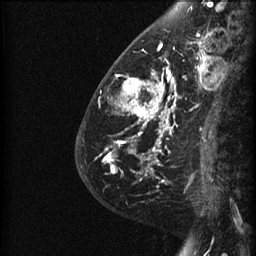
Breast MRI (dynamic contrast-enhanced), one sagittal slice; position 16 of 60 along the scan axis; dynamic contrast-enhanced series, image 2 of 3 at this slice position (ordered by acquisition); 1.5 T; TE 4.2 ms, TR 22.7 ms; 1.5 mm slice thickness; 256 × 256 image matrix. Female patient, age 48 years. Case-level facts recorded for this patient, not image findings: setting: breast cancer imaged before/during neoadjuvant chemotherapy; receptor status: triple-negative.
Structures marked on this image (semi-automatically segmented with operator editing):
- analysis volume of interest (the breast-tissue region the enhancement analysis was run in; not a lesion): bounding box <89,27,191,180> (left, top, right, bottom; pixels)
- tumour enhancement mask (voxels above the 90 % enhancement threshold inside the analysis volume of interest): <100,42,191,180>